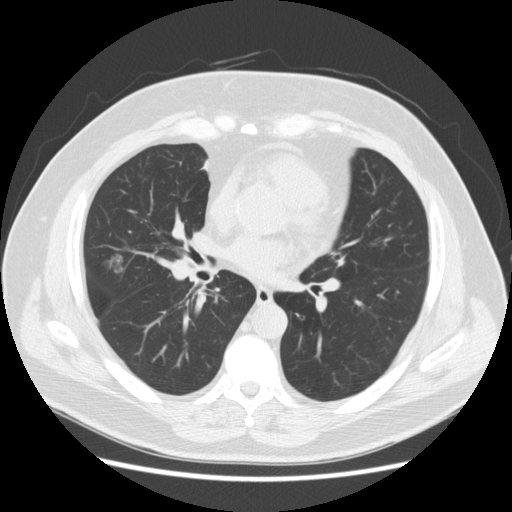
Axial slice from a low-dose chest CT screening exam, first (baseline) screen, lung window (W 1500 / L -600 HU), standard (soft-tissue) reconstruction kernel (STANDARD). Male participant, aged 67 years at enrolment.
Expert-annotated lung lesion, box from (x=90, y=249) to (x=133, y=292) px. The exam's reader record, not a measurement of the box and not confirmed to be the same lesion: non-calcified nodule or mass ≥4 mm, right middle lobe, 15 × 11 mm, smooth margins, soft tissue attenuation.